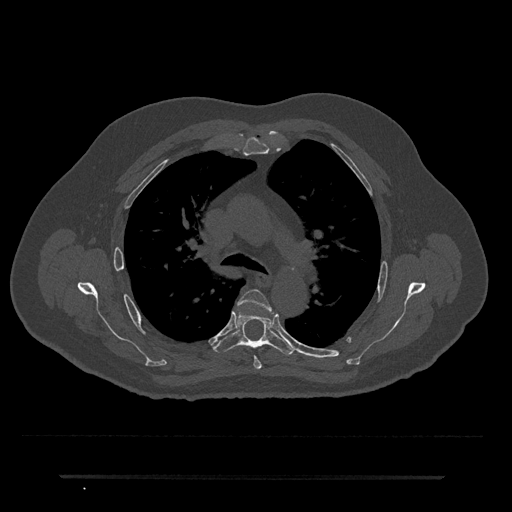
CT including the spine, one axial slice; slice 498 of 797 in the series (ordered by position); reconstruction kernel Br40s/3; 120 kVp; bone window (W 1800 / L 400 HU); 0.5 mm slice thickness; 512 × 512 image matrix, field of view 437 × 437 mm. Male patient, age 69 years. From the clinical record (not read from this slice): primary cancer: prostate.
Annotated regions visible in this slice (semi-automatically segmented with operator editing):
- T4 vertebra: box from (x=238, y=289) to (x=272, y=369) px
- T5 vertebra: (x=213, y=309)–(x=296, y=355)